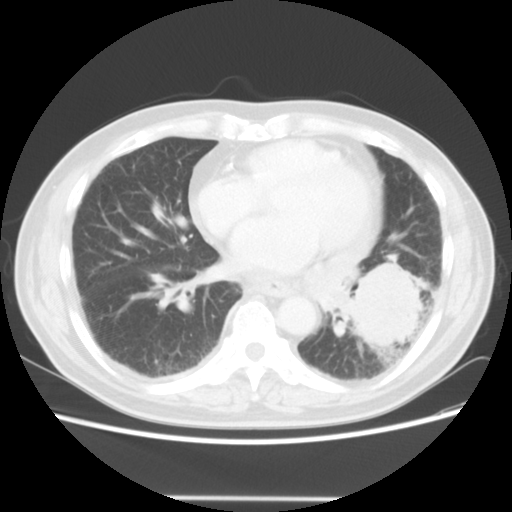
Chest CT, one axial slice; position 19 of 56 along the scan axis; reconstruction kernel STANDARD; 140 kVp; lung window (W 1500 / L -600 HU); 5 mm slice thickness; 512 × 512 image matrix, field of view 360 × 360 mm. Male patient, age 66 years. Case-level facts recorded for this patient, not image findings: clinical TNM (as recorded): T4 N3 M0; histopathological grade: G3.
Structures marked on this image (rectangle marked by the reading radiologist):
- lung tumour (recorded histology: small cell carcinoma): bounding box <339,258,434,355> (left, top, right, bottom; pixels)